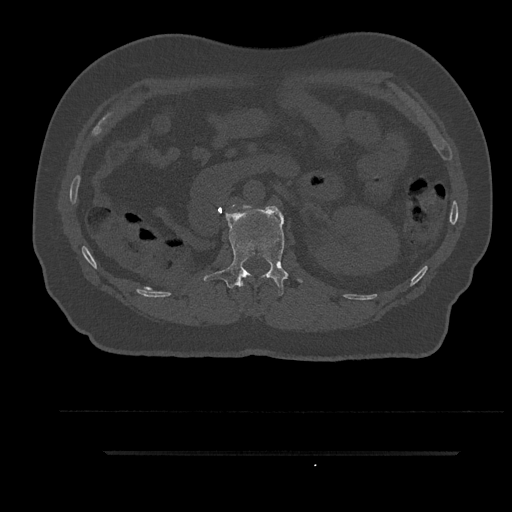
CT including the spine, one axial slice; position 179 of 797 along the scan axis; reconstruction kernel Br40s/3; 120 kVp; bone window (W 1800 / L 400 HU); 512 × 512 image matrix. Patient: male, 63 years. From the clinical record (not read from this slice): primary cancer: renal; vertebrae with lytic lesions (as recorded): T8.
Annotated regions visible in this slice (semi-automatically segmented with operator editing):
- L1 vertebra: bounding box (x1, y1, x2, y2) in pixels: (204, 206, 302, 296)
- L2 vertebra: (232, 205, 234, 207)
- T12 vertebra: (240, 281, 244, 287)